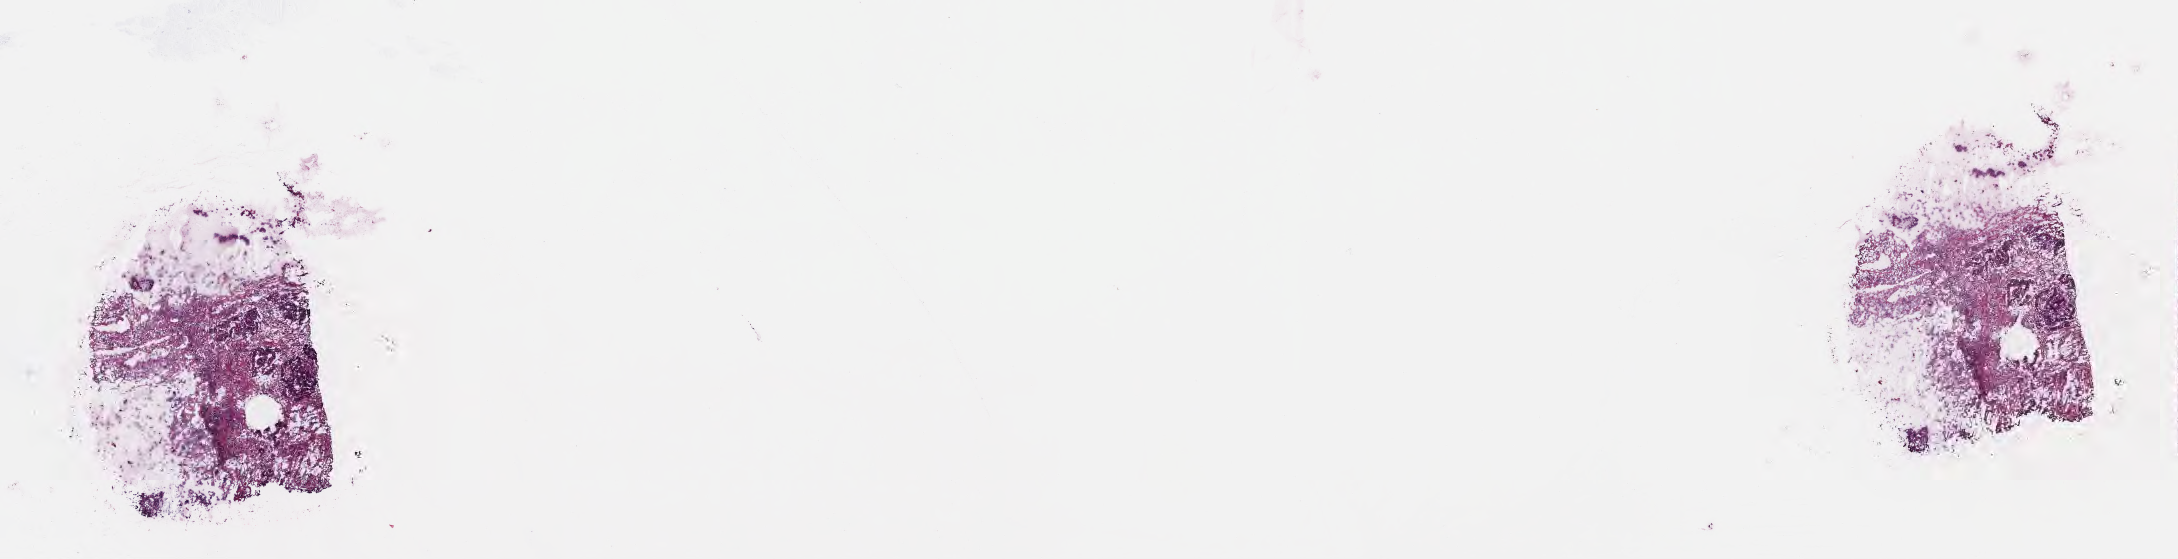
Digitized hematoxylin and eosin (H&E)-stained section — whole scanned area (about 17.6 x 4.5 mm) shown as a low-resolution overview; cryosection; specimen: primary tumor; site: rectosigmoid junction. Female, age 53 years at initial diagnosis. Tumor grade: G2 (moderately differentiated). Pathologist review of this section (percent, as recorded): tumor cells 70%, tumor nuclei 70%, stromal cells 25%, necrosis 1%, normal cells 4%. Infiltration values recorded for this section: lymphocyte infiltration 5%, monocyte infiltration 5%, neutrophil infiltration 8%.
• AJCC pathologic stage: Stage IIIB
• diagnosis: Adenocarcinoma, NOS